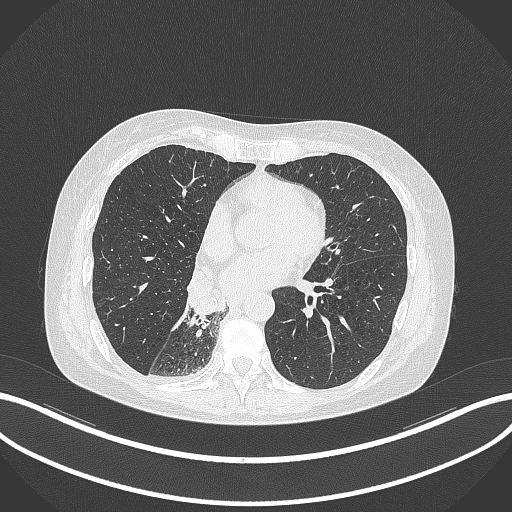
Chest CT, one axial slice. Position 131 of 329 along the scan axis. 120 kVp. Lung window (W 1500 / L -600 HU). 1 mm slice thickness. 512 × 512 image matrix, field of view 400 × 400 mm. Patient: female, 63 years. From the clinical record (not read from this slice): clinical TNM (as recorded): T1c N0 M0.
Outlined on this slice (bounding box drawn by a radiologist):
- lung tumour (recorded histology: adenocarcinoma): box from (x=179, y=268) to (x=226, y=324) px